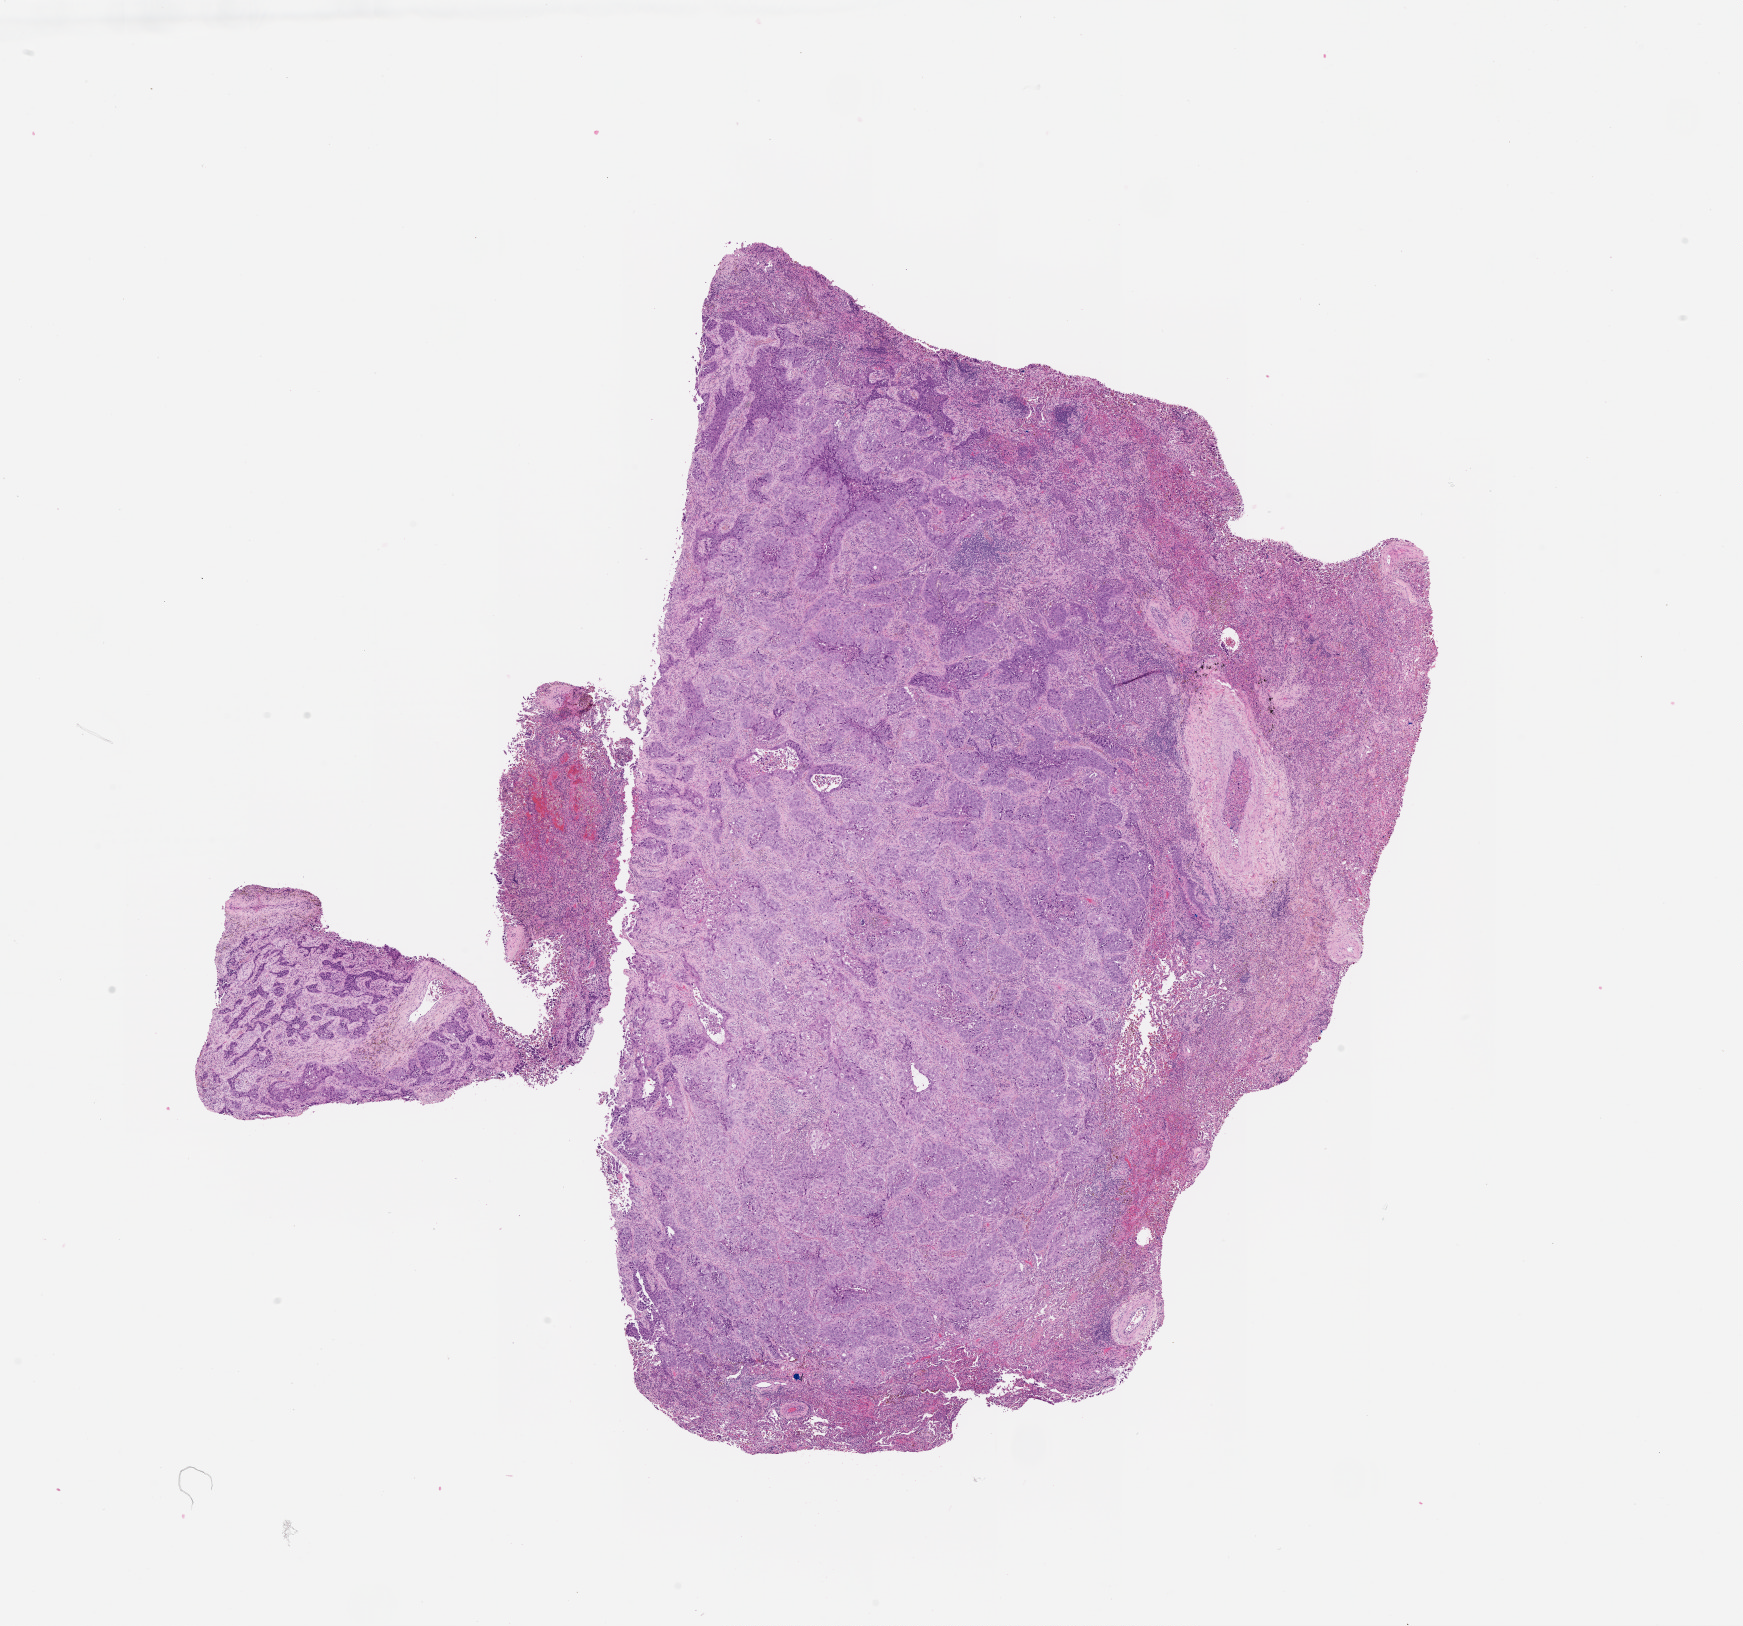
Digitized H&E tissue section (whole slide) — whole scanned area (about 14.0 x 13.1 mm) shown as a low-resolution overview; lung, tumour tissue. 67-year-old male patient.
- patient diagnosis (cohort enrolment): squamous cell carcinoma (lung)